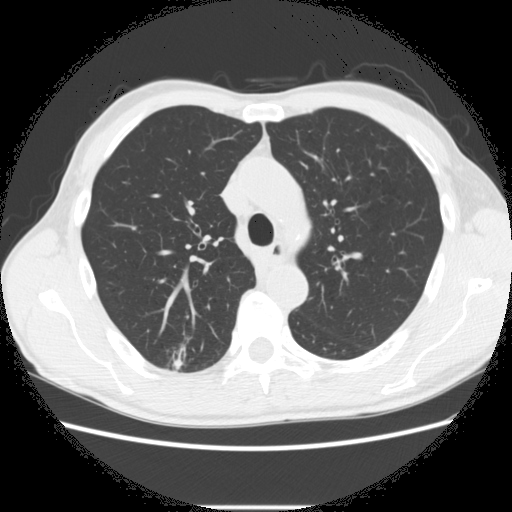
Low-dose screening chest CT, one axial slice; position 199 of 282 along the scan axis; reconstruction kernel STANDARD; lung window (W 1500 / L -600 HU); 512 × 512 image matrix, field of view 360 × 360 mm.
Annotated regions visible in this slice (outlined manually by an expert reader):
- lesion 1 (tumor, upper lobe of right lung): bounding box (x1, y1, x2, y2) in pixels: (173, 359, 183, 370)